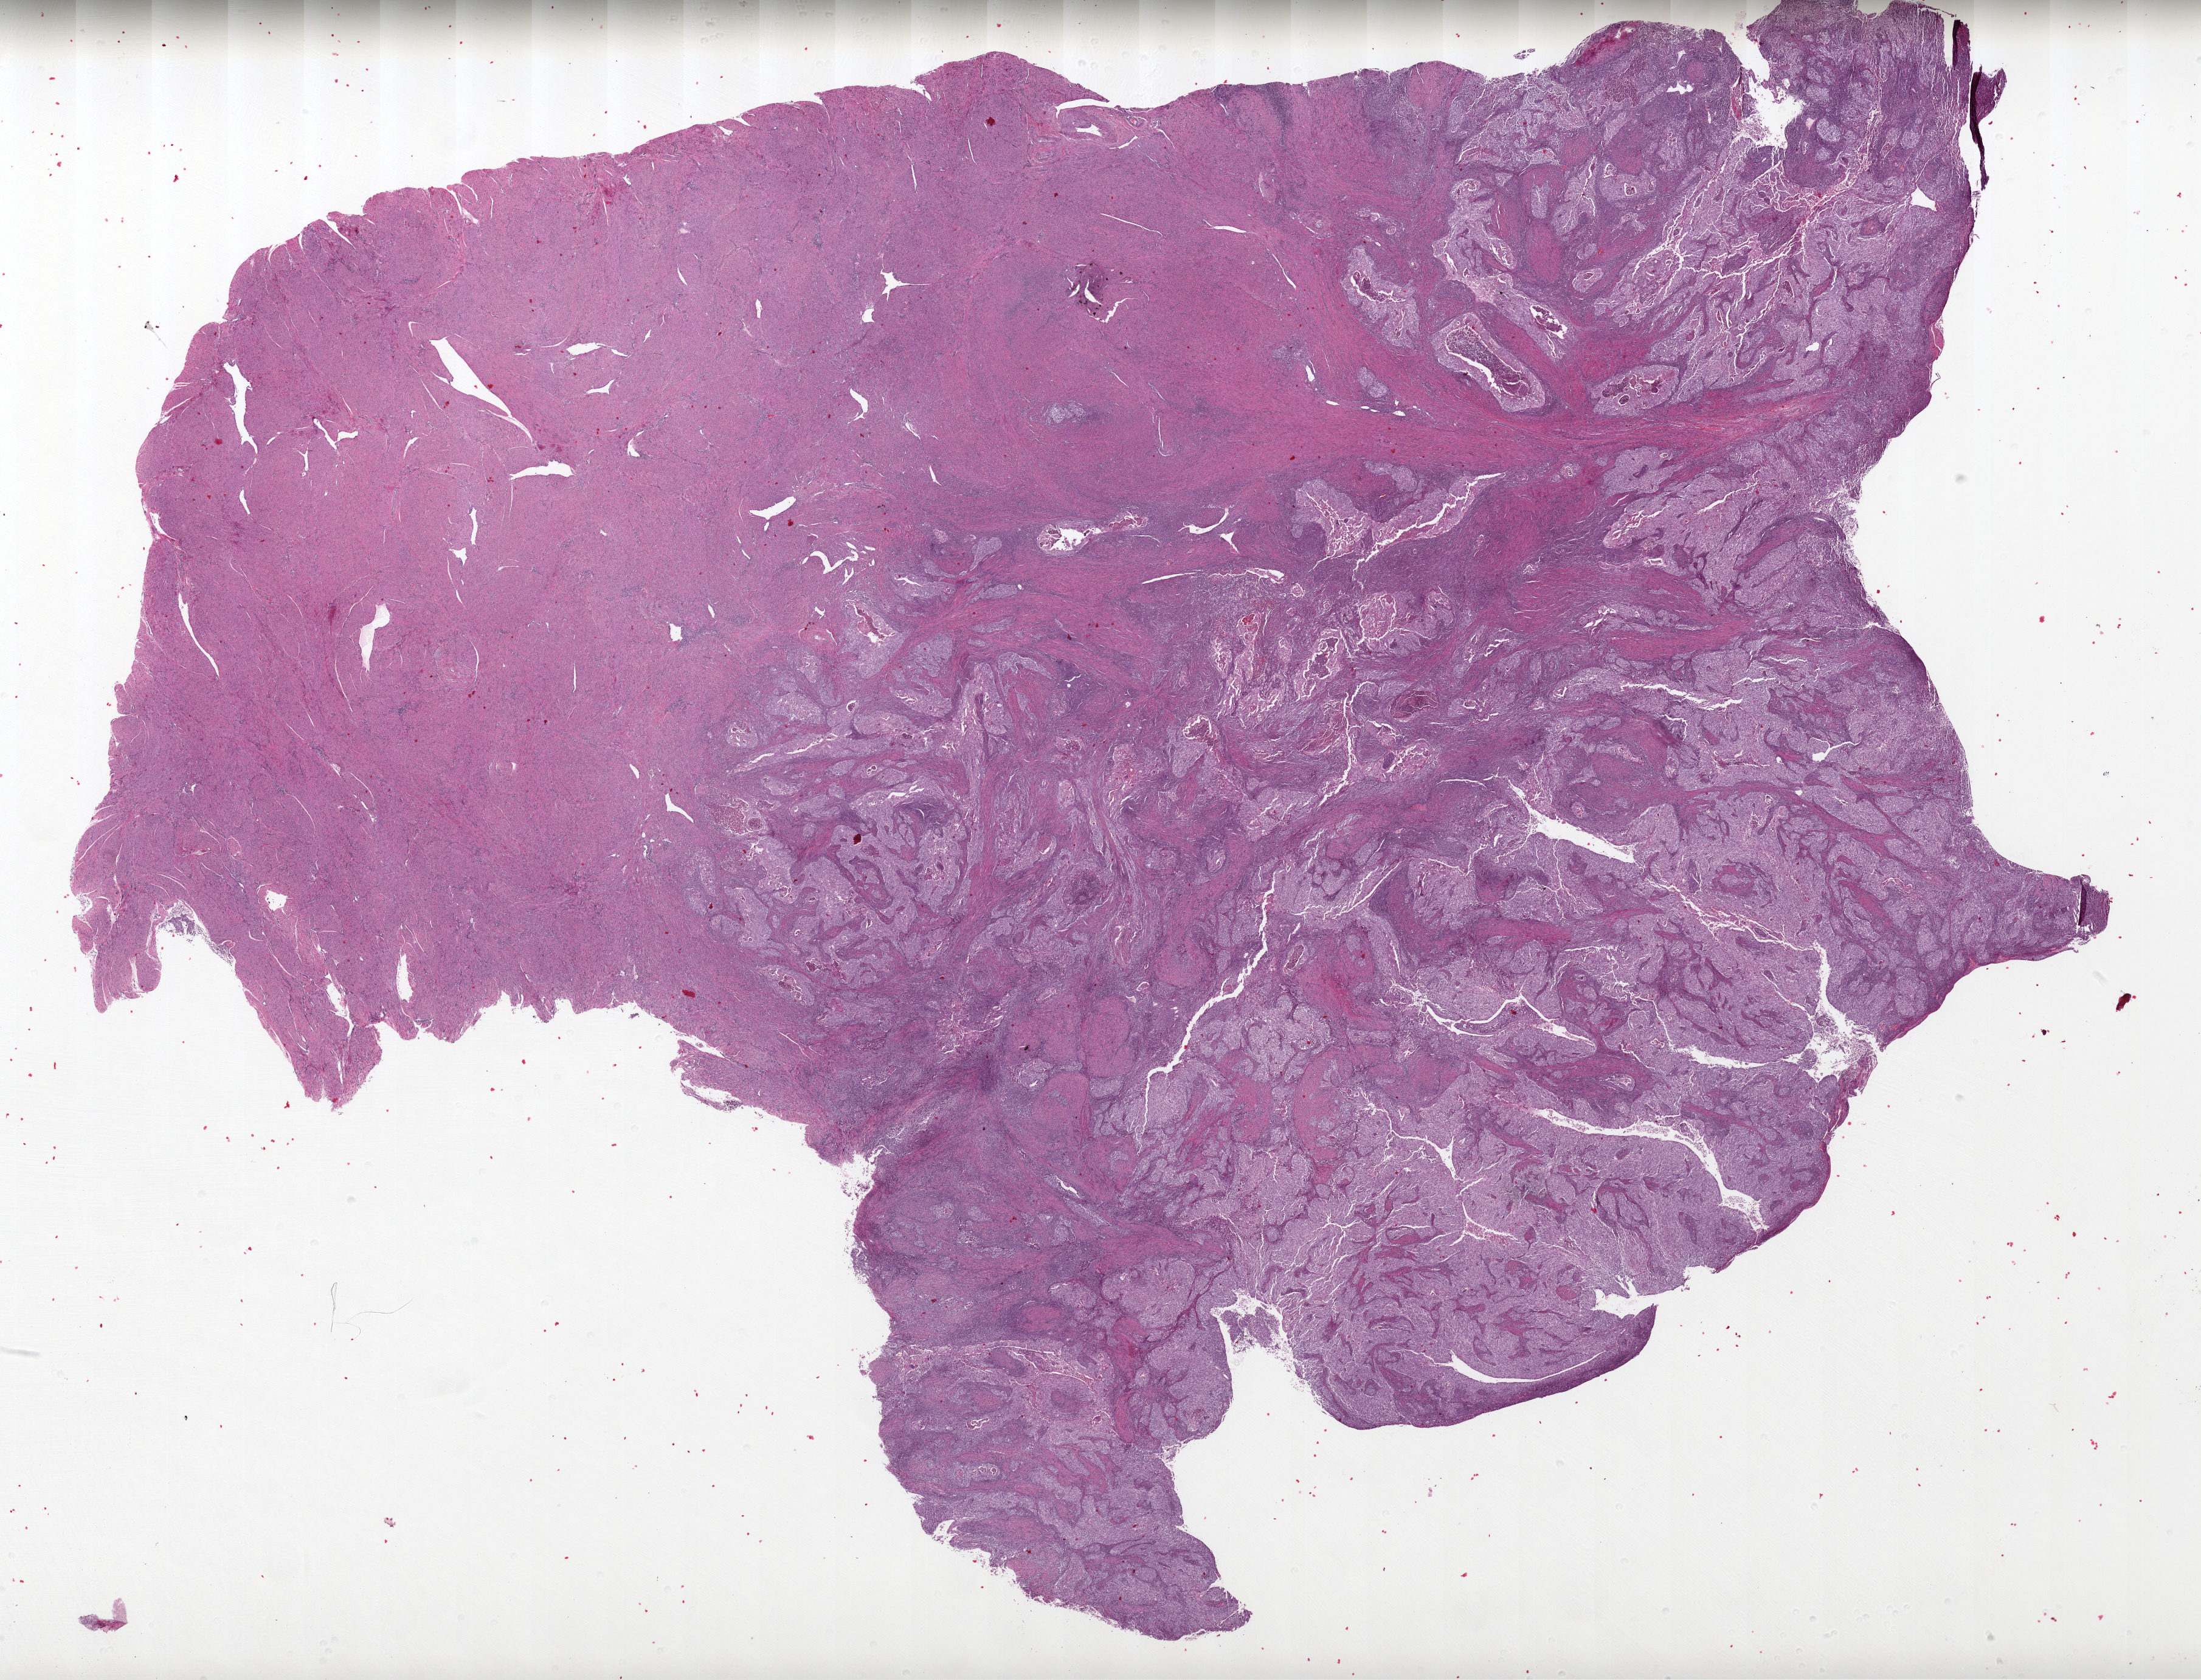
Whole-slide histology image, H&E-stained — low-resolution overview of the scanned area, about 28.8 x 22.0 mm, formalin-fixed paraffin-embedded (FFPE) diagnostic section, sample: primary tumour, uterus. Female patient; age at initial diagnosis 45 years. Histologic grade: G3 (poorly differentiated).
• pathologic diagnosis: Endometrioid adenocarcinoma, NOS (endometrium)
• FIGO stage: IIIC1